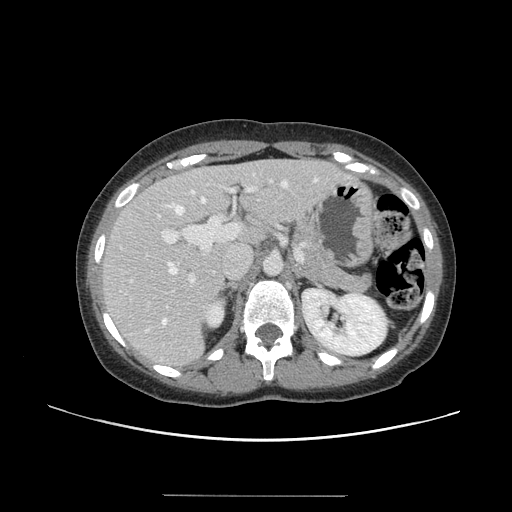
Contrast-enhanced abdominal CT, one axial slice. Position 88 of 144 along the scan axis. 120 kVp. Intravenous contrast given. Soft-tissue window (W 400 / L 40 HU). 512 × 512 image matrix. Female patient, age 53 years. Case-level facts recorded for this patient, not image findings: diagnosis: colorectal cancer liver metastases, imaged before liver resection; multiple liver metastases: yes; largest metastasis: 1.1 cm; disease in both lobes: no.
Outlined on this slice (outlined manually by an expert reader):
- hepatic veins: bounding box (x1, y1, x2, y2) in pixels: (162, 179, 317, 324)
- liver: (102, 160, 347, 367)
- planned liver remnant (the part of the liver to remain after resection): (103, 160, 314, 297)
- portal vein (with intrahepatic branches): (129, 179, 301, 284)